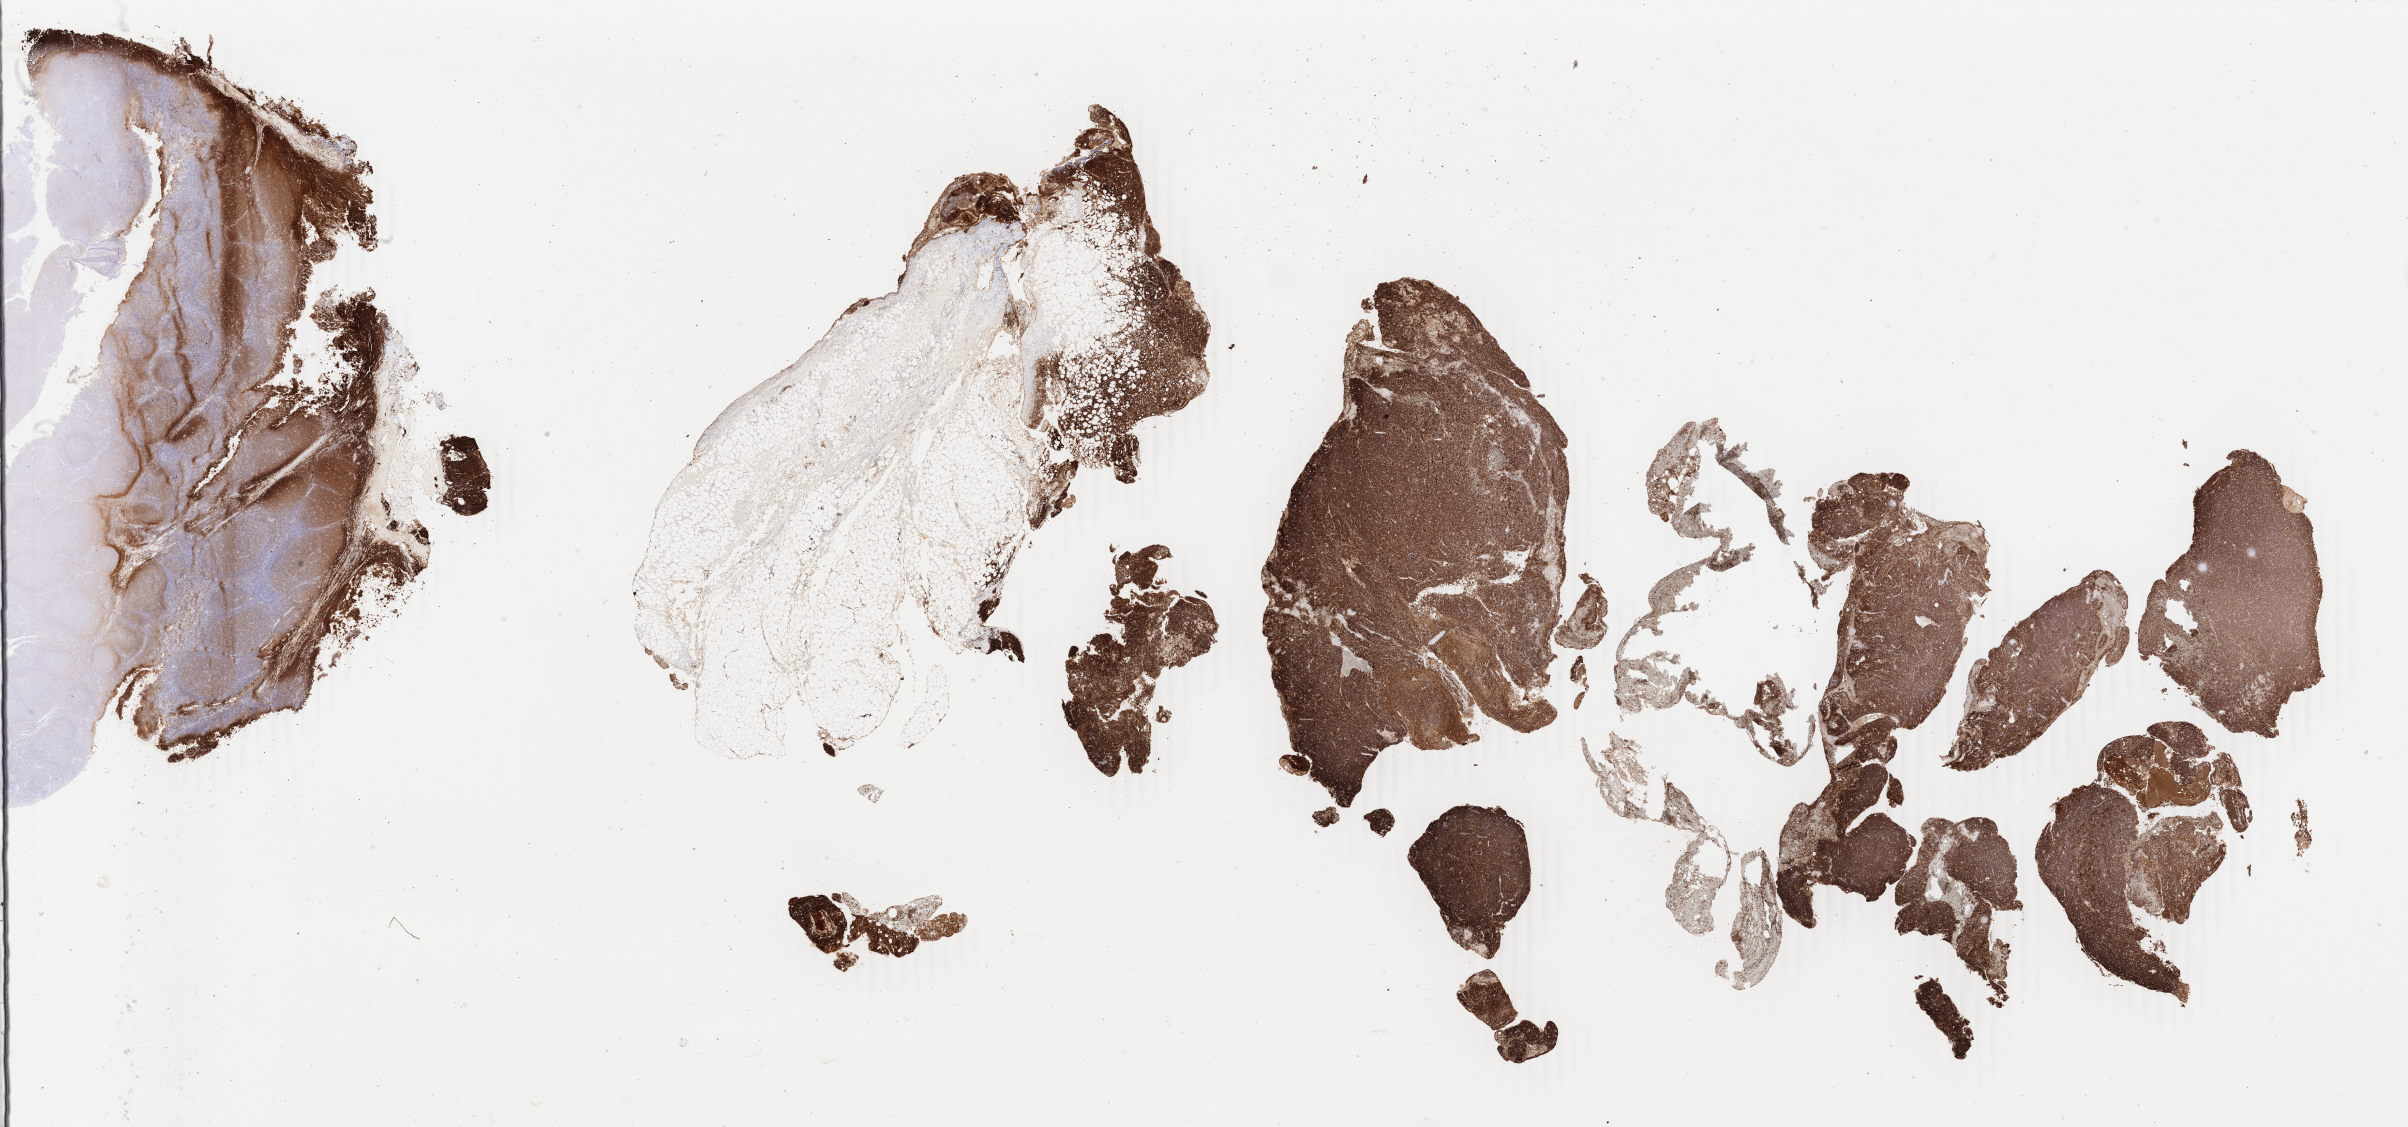
Immunohistochemistry (IHC) whole-slide image stained for CD20 — a low-resolution overview of the entire scanned area, about 38.3 x 17.9 mm. Specimen: tumor tissue. Anatomic site: abdominal lymph node. Patient: male, age 27 years.
Diagnosis: Burkitt lymphoma, NOS.